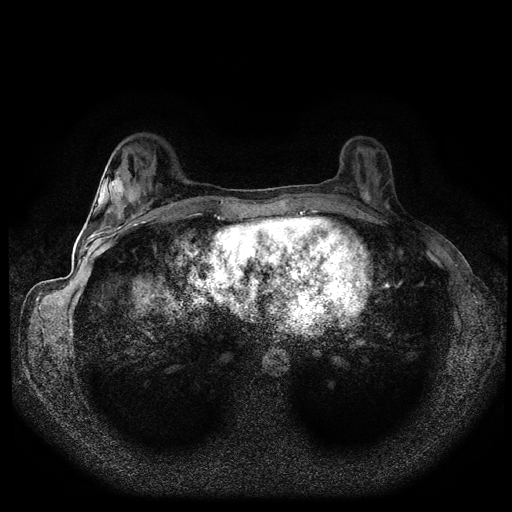
Breast MRI (dynamic contrast-enhanced, multi-phase), one axial slice. Position 34 of 108 along the scan axis. Dynamic contrast-enhanced series, time point 2 of 5 at this slice position (early post-contrast). 1.5 T. TE 2.7 ms, TR 5.5 ms. 2 mm slice thickness. 512 × 512 image matrix, field of view 320 × 320 mm. Female patient, age 36 years.
Annotated regions visible in this slice (semi-automatically segmented with operator editing):
- breast lesion (labelled benign in the annotation): box from (x=107, y=171) to (x=130, y=202) px